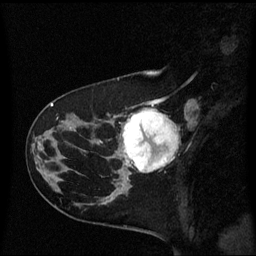
Breast MRI (dynamic contrast-enhanced), one sagittal slice; position 21 of 60 along the scan axis; dynamic contrast-enhanced series, image 2 of 3 at this slice position (ordered by acquisition); 1.5 T; TE 4.2 ms, TR 8.4 ms; 2 mm slice thickness; 256 × 256 image matrix. Female patient, age 41 years. From the clinical record (not read from this slice): setting: breast cancer imaged before/during neoadjuvant chemotherapy; receptor status: triple-negative.
Annotated regions visible in this slice (semi-automatic segmentation, software-assisted and operator-edited):
- analysis volume of interest (the breast-tissue region the enhancement analysis was run in; not a lesion): bounding box (x1, y1, x2, y2) in pixels: (116, 108, 178, 177)
- tumour enhancement mask (voxels above the 70 % enhancement threshold inside the analysis volume of interest): (122, 110, 178, 173)